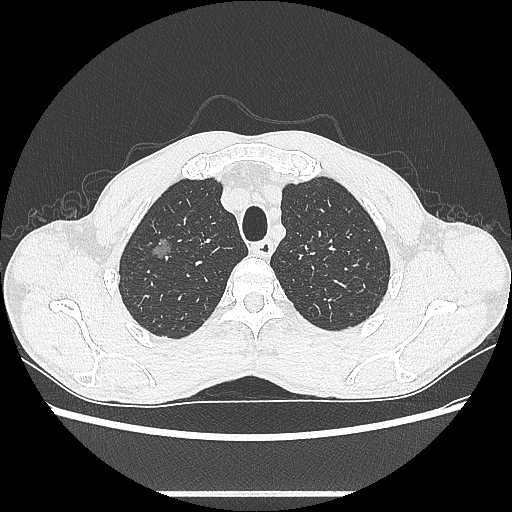
Chest CT, one axial slice. Position 496 of 601 along the scan axis. Lung window (W 1500 / L -600 HU). 0.62 mm slice thickness. 512 × 512 image matrix, field of view 357 × 357 mm. Male patient, age 54 years. Case-level facts recorded for this patient, not image findings: clinical TNM (as recorded): T1a N0 M0.
Outlined on this slice (bounding box drawn by a radiologist):
- lung tumour (recorded histology: adenocarcinoma): bounding box <148,231,177,267> (left, top, right, bottom; pixels)